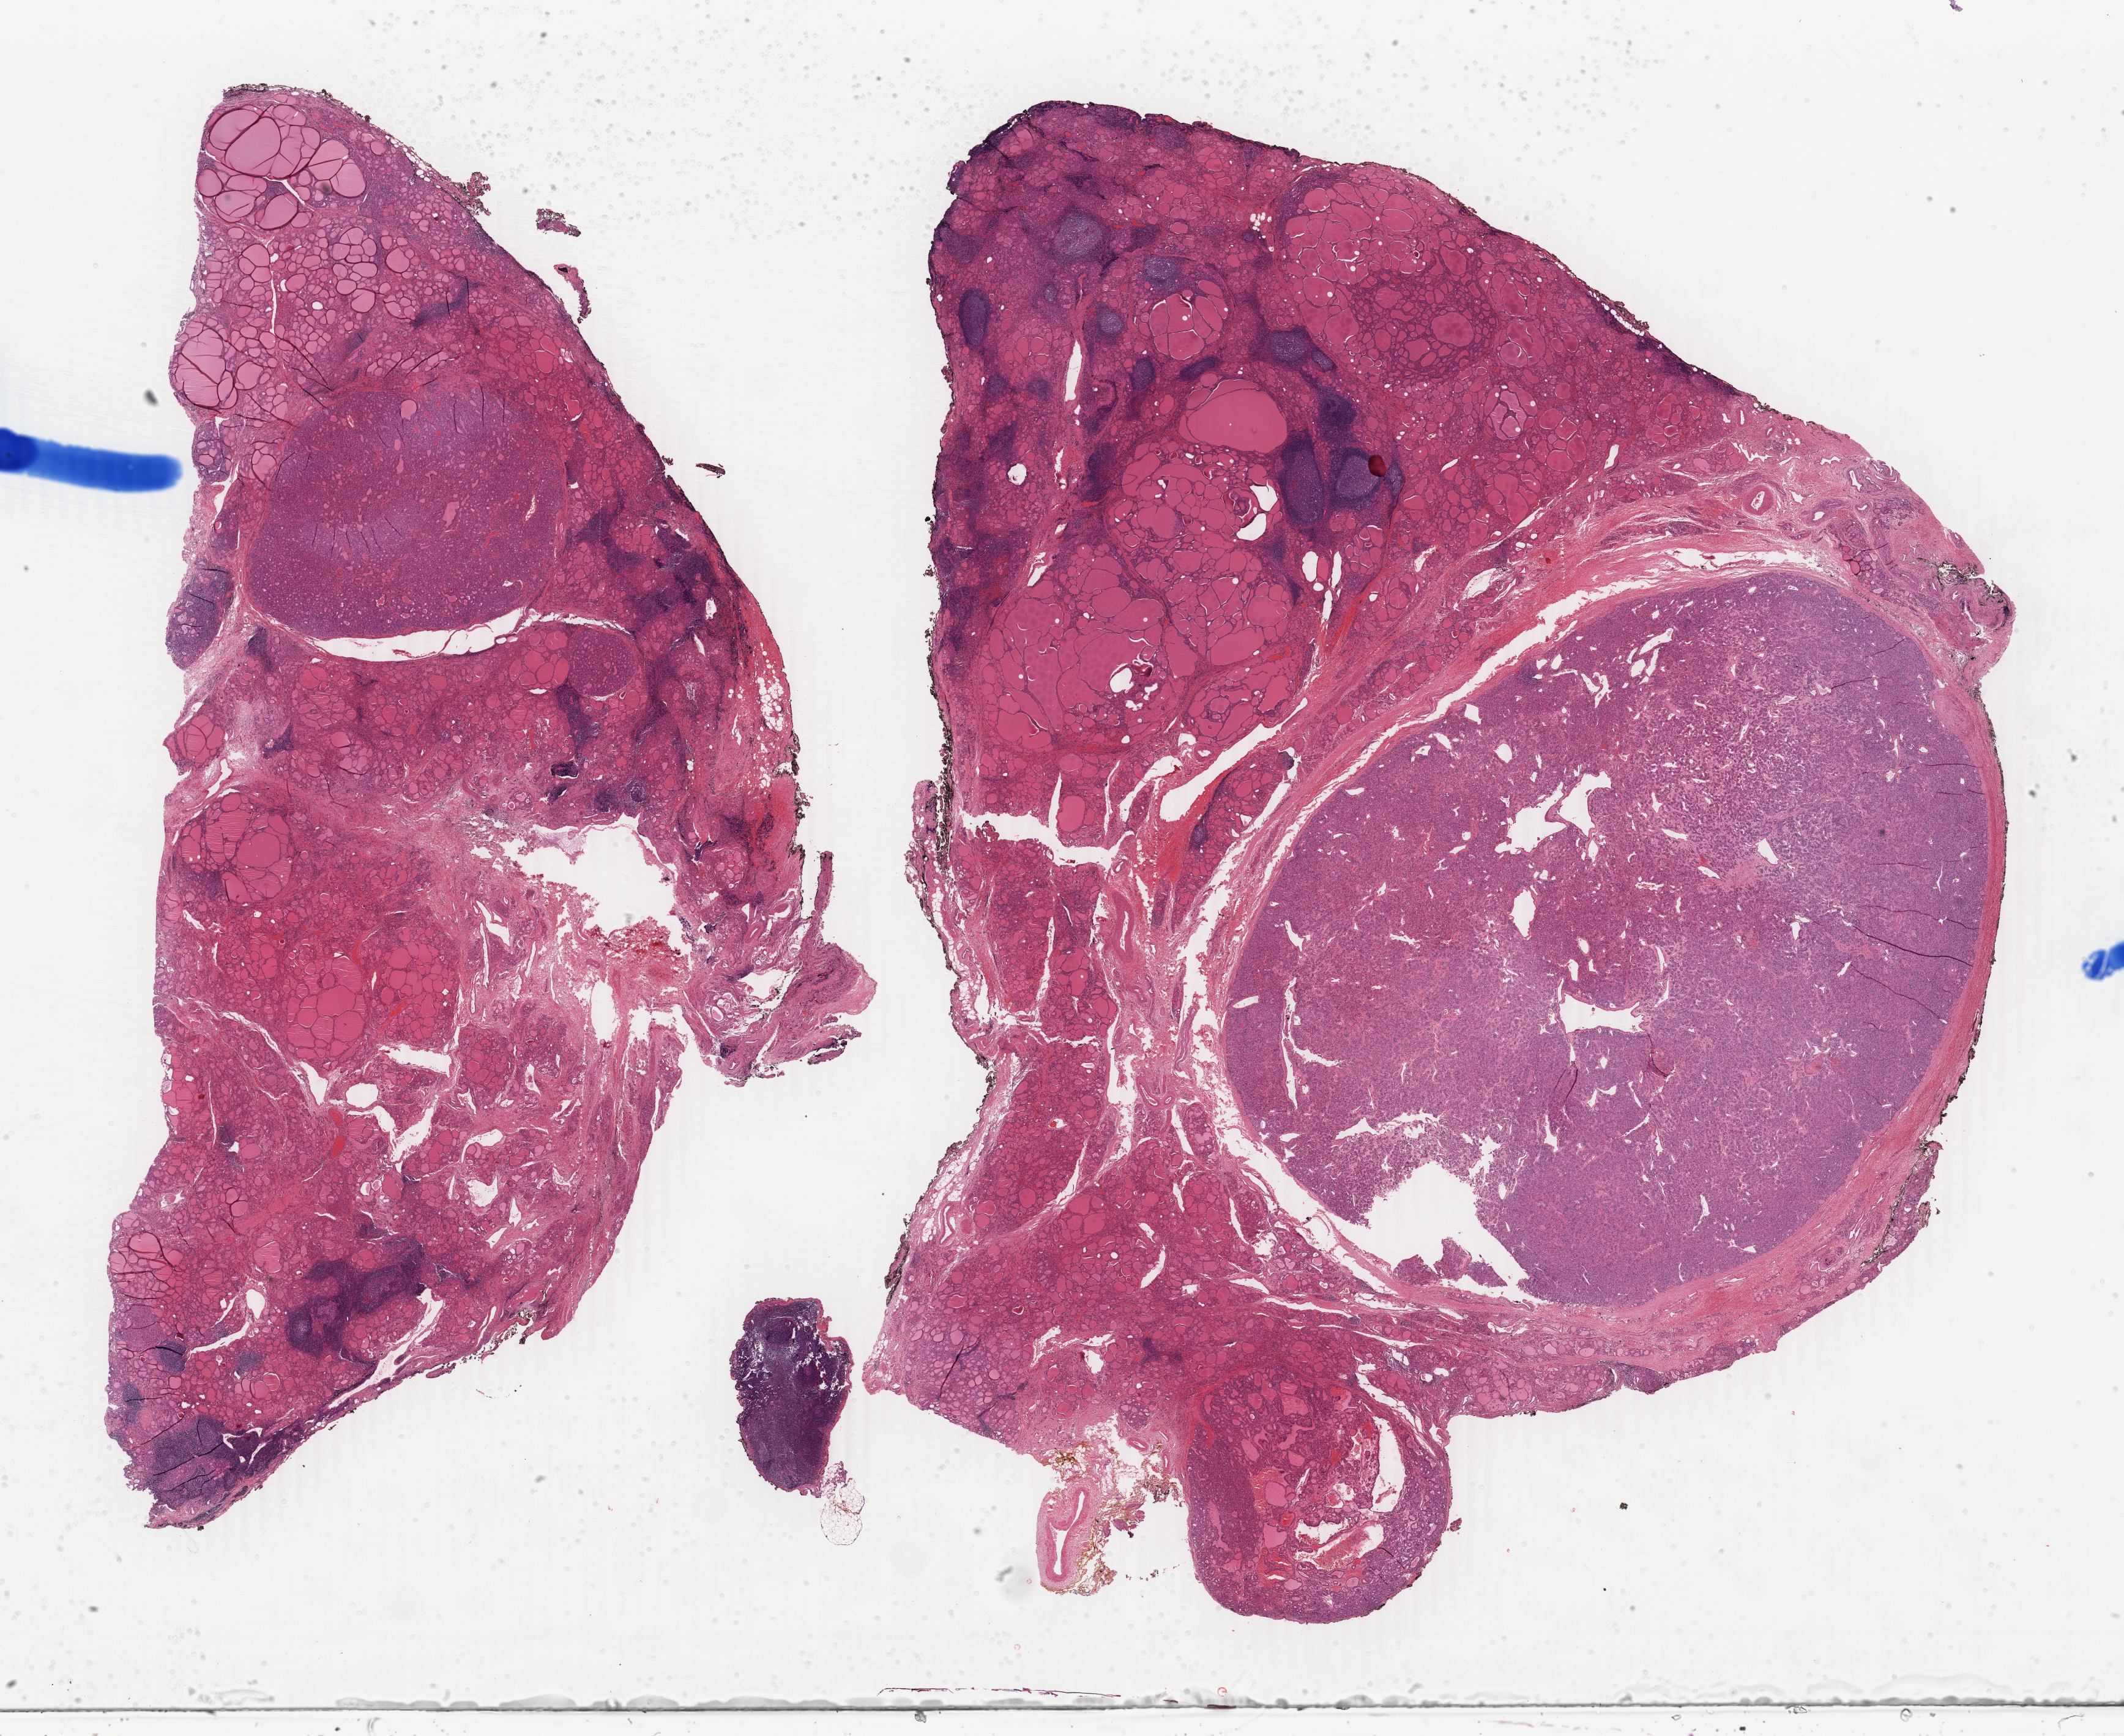
Digitized Hematoxylin and eosin (H&E) stained tissue section (whole slide) — whole scanned area (about 27.6 x 22.6 mm, acquisition: 40x scan) shown as a low-resolution overview. Formalin-fixed paraffin-embedded (FFPE) diagnostic section. Thyroid, primary tumour sample. Female patient; age at initial diagnosis 56 years.
AJCC pathologic stage: I (7th edition). Lymph nodes positive (case pathology): 0 of 9 examined. Pathologic diagnosis: Papillary adenocarcinoma, NOS (thyroid gland). TNM: T1 N0 M0.